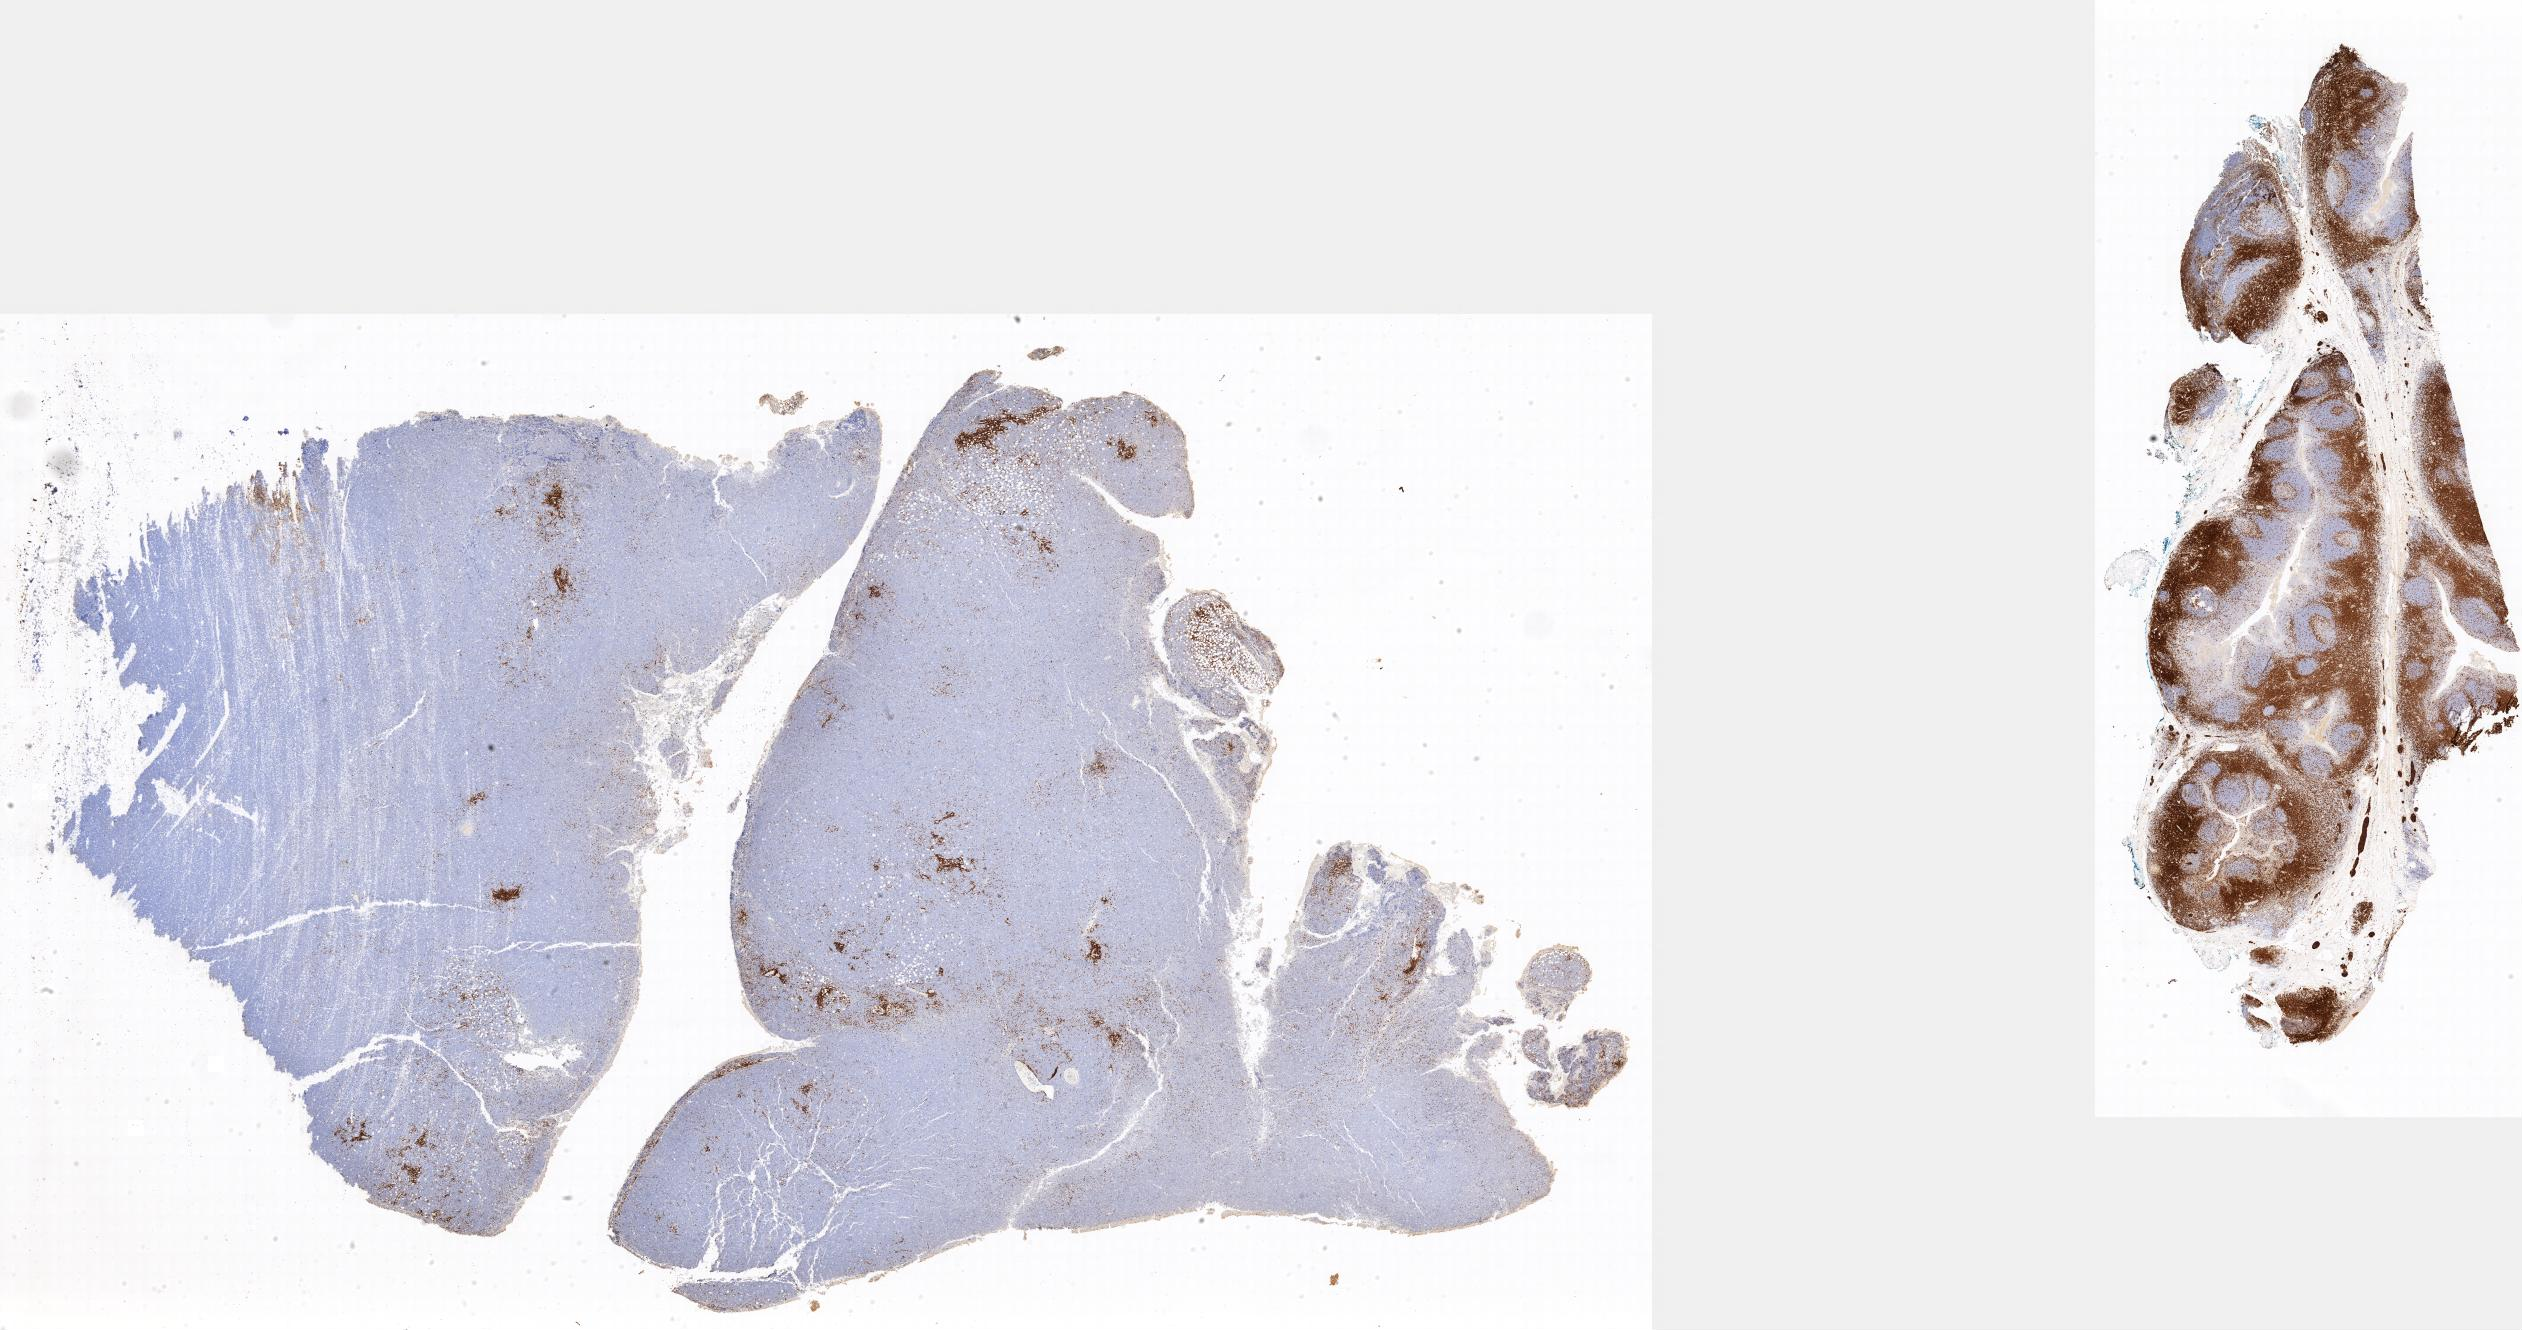
IHC for CD3, whole-slide image — low-resolution overview of the scanned area. Specimen: tumor tissue. Site: peritoneum. Patient: male, age at initial diagnosis 9 years.
Histologic diagnosis: Burkitt lymphoma, NOS.